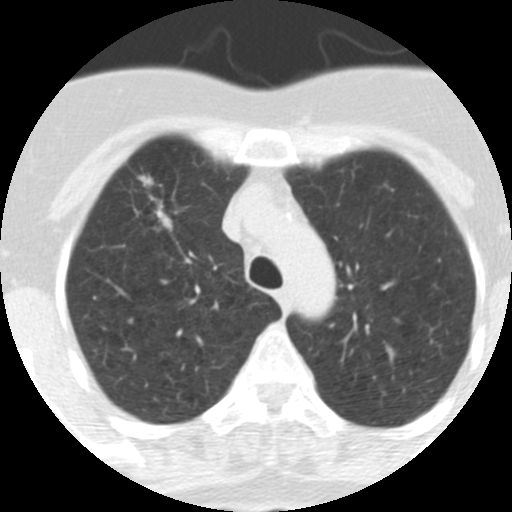
Low-dose screening chest CT, one axial slice; position 245 of 313 along the scan axis; reconstruction kernel STANDARD; lung window (W 1500 / L -600 HU); 2.5 mm slice thickness; 512 × 512 image matrix.
Structures marked on this image (expert manual segmentation):
- lesion 1 (tumor, upper lobe of right lung): box from (x=138, y=175) to (x=172, y=231) px